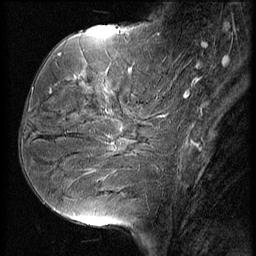
Breast MRI (dynamic contrast-enhanced), one sagittal slice; slice 20 of 56 in the series (ordered by position); 3 images stored at this slice position (order not interpretable as contrast timing); 1.5 T; TE 4.2 ms, TR 9 ms; 2.5 mm slice thickness; 256 × 256 image matrix, field of view 180 × 180 mm. Female patient, age 51 years. From the clinical record (not read from this slice): setting: breast cancer imaged before/during neoadjuvant chemotherapy; receptor status: HR-positive, HER2-negative.
Structures marked on this image (semi-automatic segmentation, software-assisted and operator-edited):
- analysis volume of interest (the breast-tissue region the enhancement analysis was run in; not a lesion): bounding box [x1, y1, x2, y2] px = [23, 56, 156, 165]
- tumour enhancement mask (voxels above the 140 % enhancement threshold inside the analysis volume of interest): [78, 70, 129, 107]